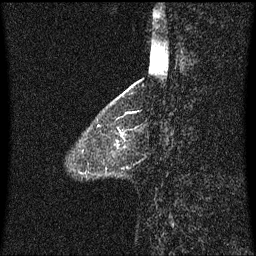
Breast MRI (dynamic contrast-enhanced), one sagittal slice; position 16 of 60 along the scan axis; dynamic contrast-enhanced series, image 2 of 3 at this slice position (ordered by acquisition); 1.5 T; TE 4.2 ms, TR 8.4 ms; 2 mm slice thickness; 256 × 256 image matrix. Female patient, age 58 years.
Structures marked on this image (semi-automatically segmented with operator editing):
- analysis volume of interest (the breast-tissue region the enhancement analysis was run in; not a lesion): bounding box (x1, y1, x2, y2) in pixels: (100, 131, 127, 150)
- tumour enhancement mask (voxels above the 70 % enhancement threshold inside the analysis volume of interest): (120, 132, 123, 136)